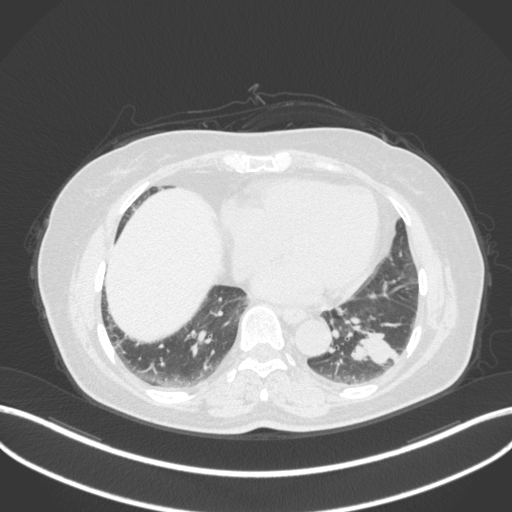
Chest CT, one axial slice; slice 130 of 307 in the series (ordered by position); 120 kVp; lung window (W 1500 / L -600 HU); 1 mm slice thickness; 512 × 512 image matrix, field of view 400 × 400 mm. Female patient, age 59 years. From the clinical record (not read from this slice): clinical TNM (as recorded): T2a N0 M0.
Outlined on this slice (bounding box drawn by a radiologist):
- lung tumour (recorded histology: adenocarcinoma): bounding box (x1, y1, x2, y2) in pixels: (347, 325, 402, 368)